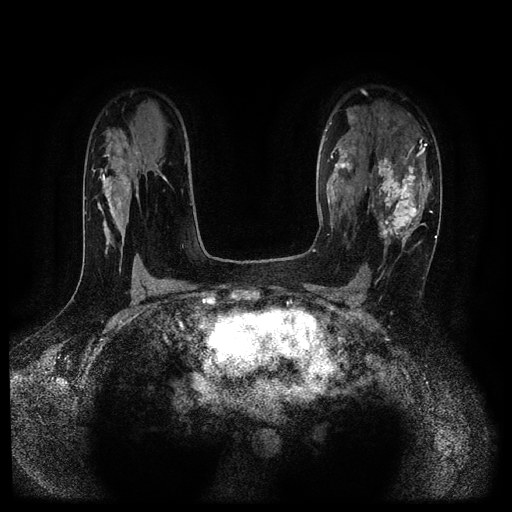
Breast MRI (dynamic contrast-enhanced, multi-phase), one axial slice. Slice 69 of 116 in the series (ordered by position). Dynamic contrast-enhanced series, time point 2 of 5 at this slice position (early post-contrast). 1.5 T. TE 2.7 ms, TR 5.4 ms. 2.2 mm slice thickness. 512 × 512 image matrix. Female patient, age 43 years.
Outlined on this slice (semi-automatically segmented with operator editing):
- breast lesion (labelled 'tumour' in the annotation; benign lesions carry a separate 'benign' label): bounding box [x1, y1, x2, y2] px = [370, 157, 428, 253]
- breast lesion (labelled benign in the annotation): [326, 148, 355, 203]